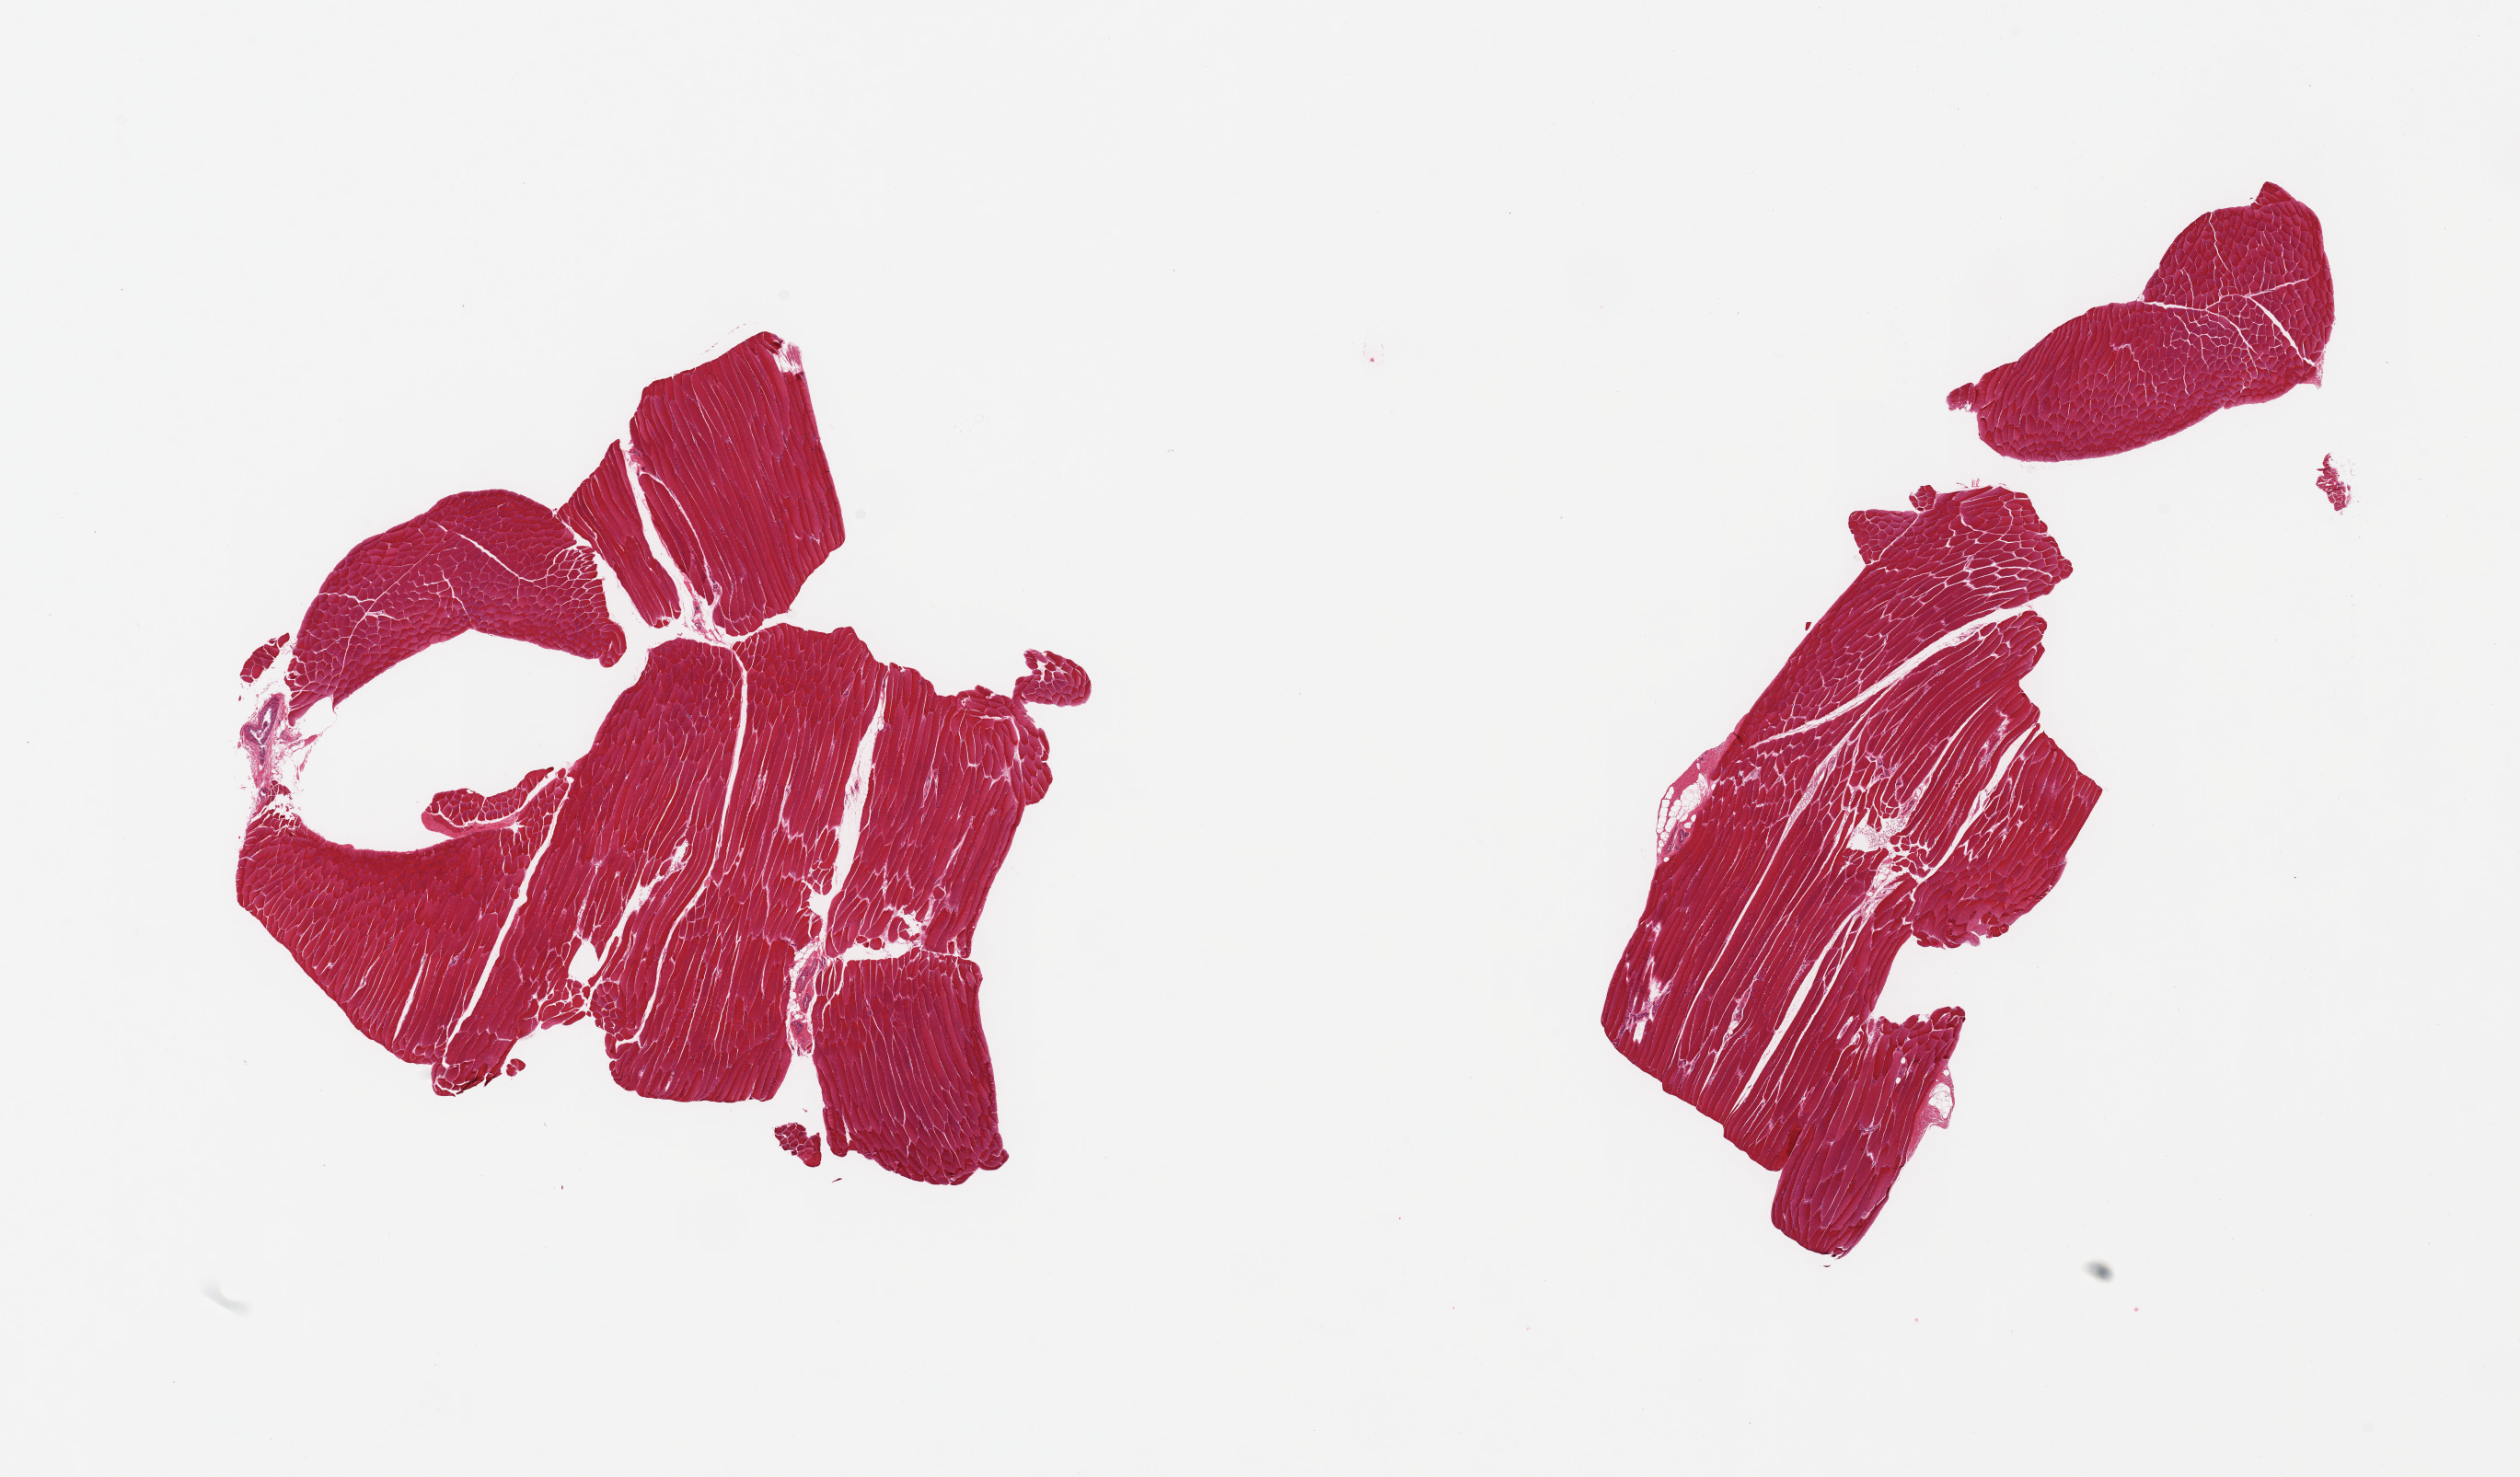
Haematoxylin and eosin whole-slide image, brightfield — whole scanned area (about 21.7 x 12.7 mm) shown as a low-resolution overview; PAXgene-fixed paraffin-embedded (PFPE) section; section of skeletal muscle (target tissue); tissue donor sample. Donor sex: male.
- reviewer comment on this tissue sample: 2 pieces; skeletal muscle with trivial fat